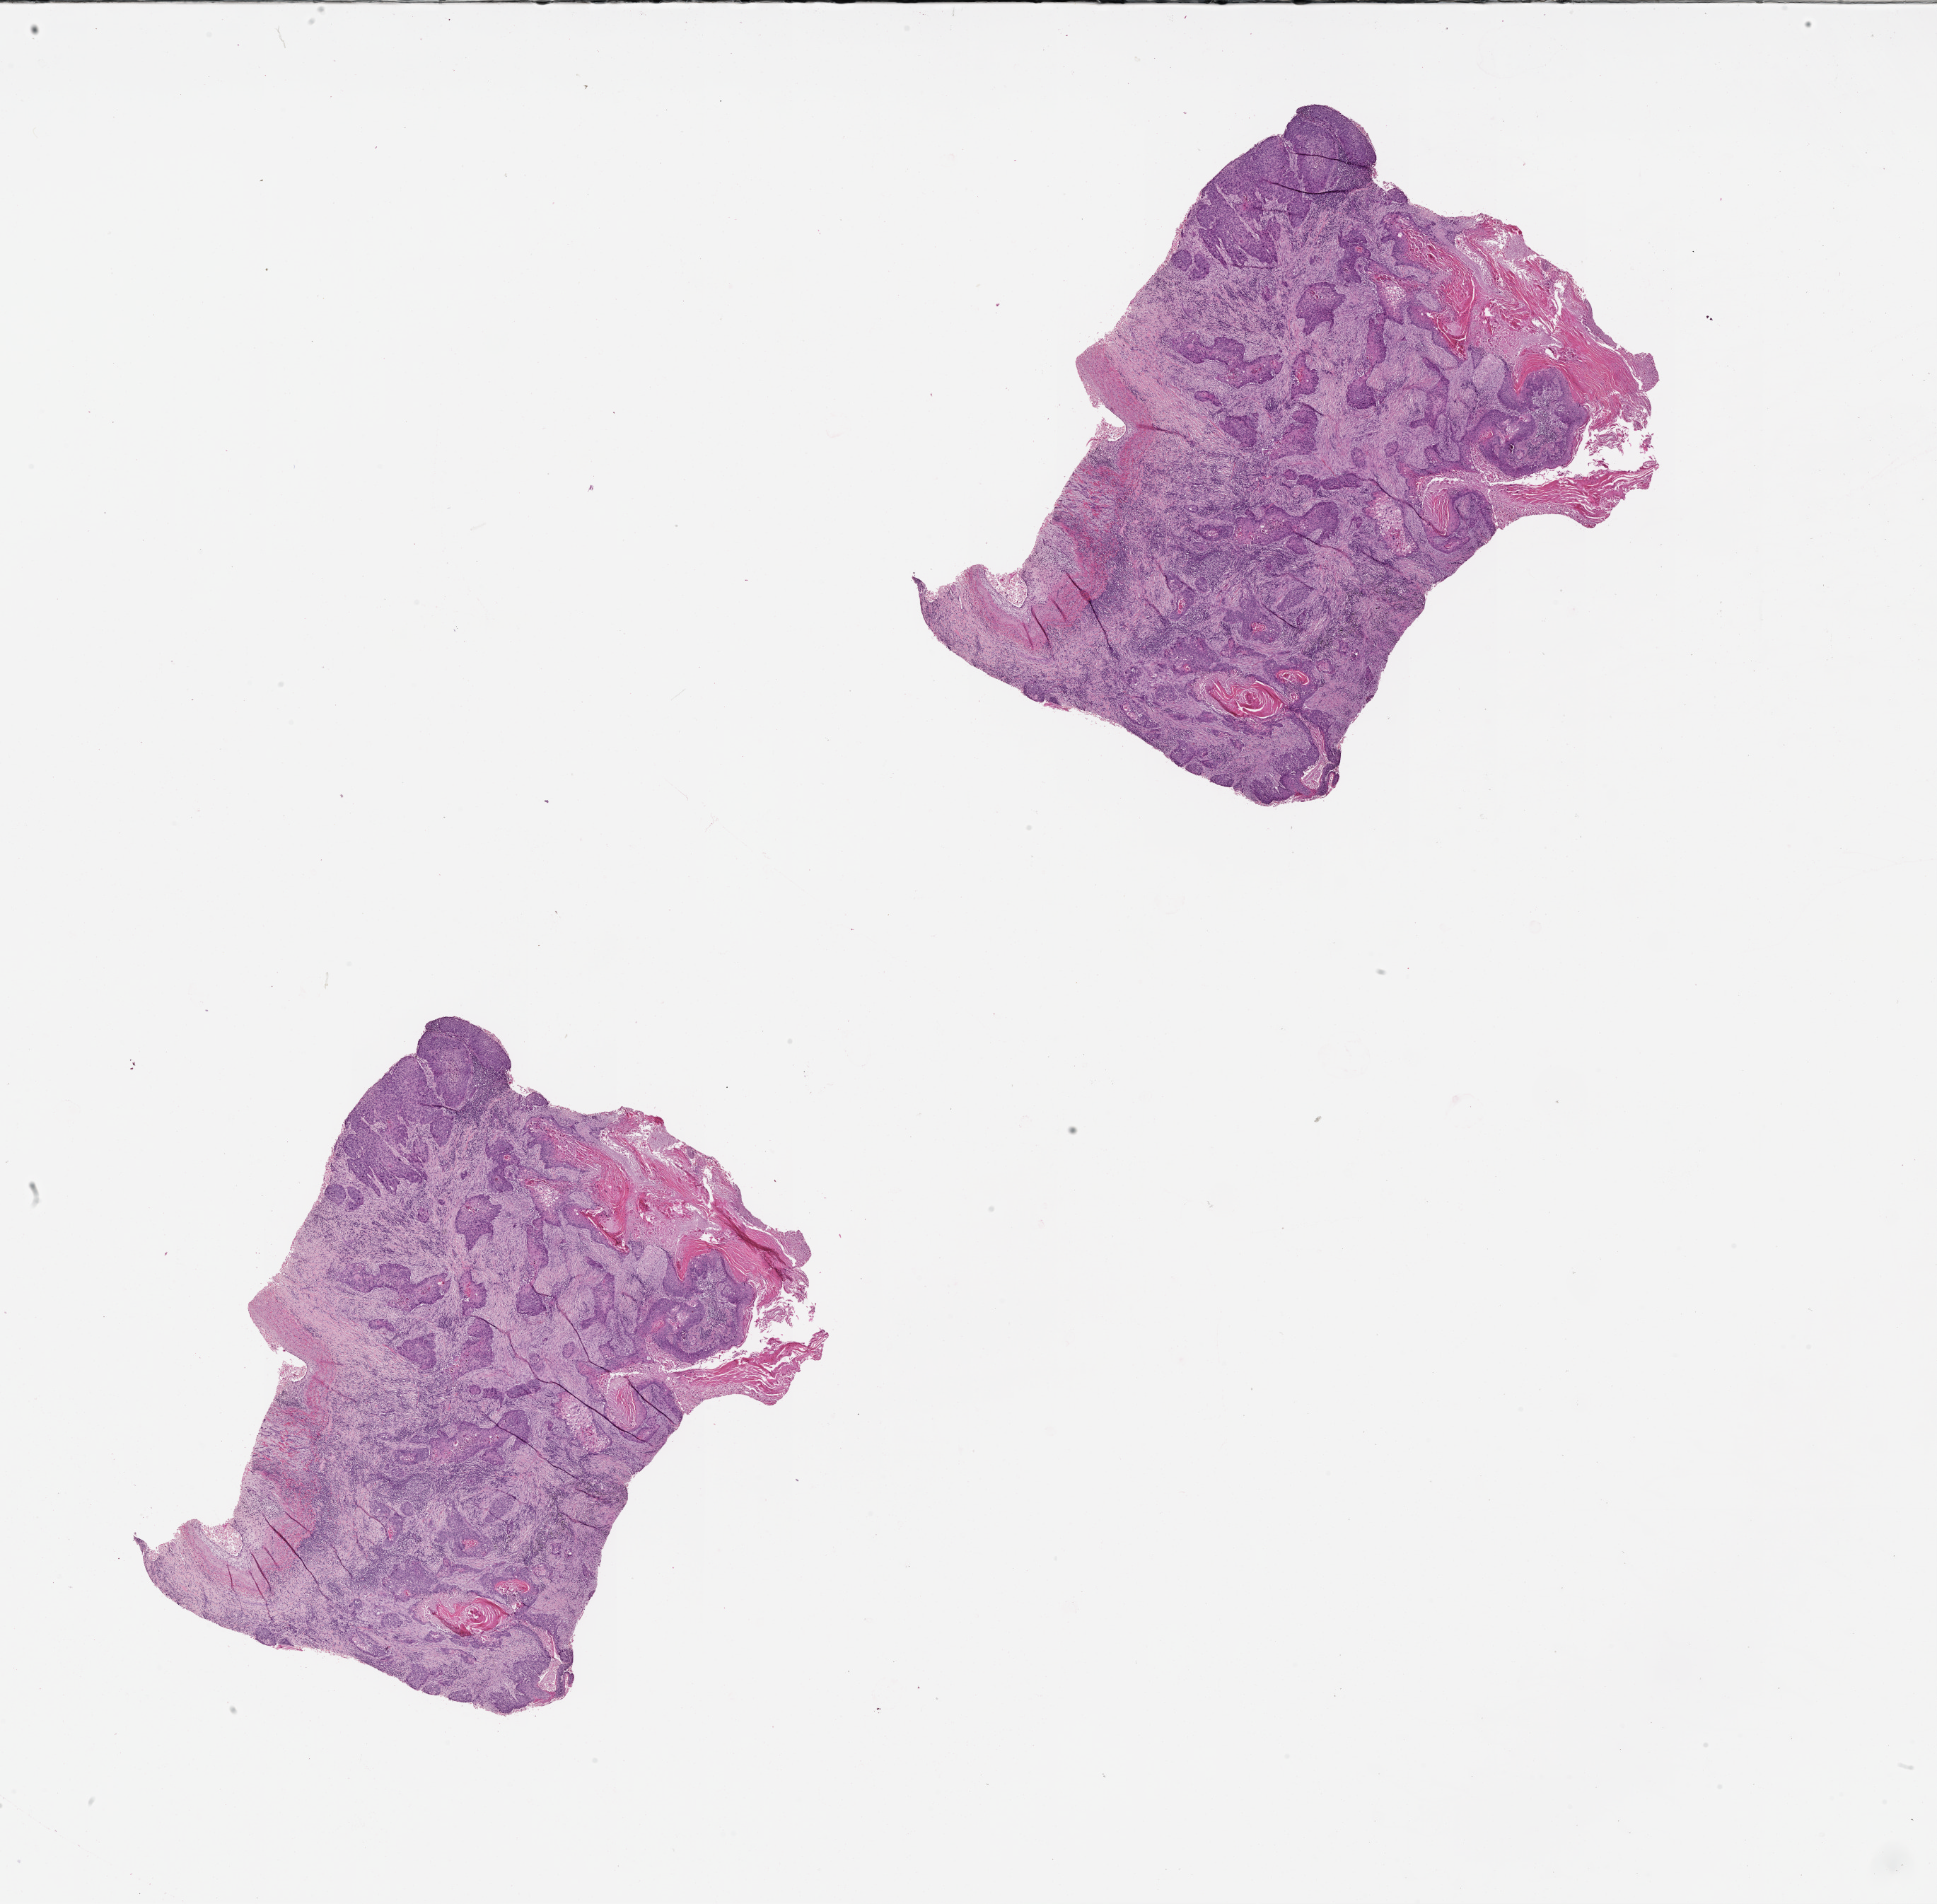
Digitized H&E-stained tissue section (whole slide) — low-resolution overview of the scanned area, about 22.0 x 21.7 mm (slide scanned at 20x), tumour tissue sample, lung. Female, 60 y/o.
Patient diagnosis (cohort enrolment): squamous cell carcinoma (lung).